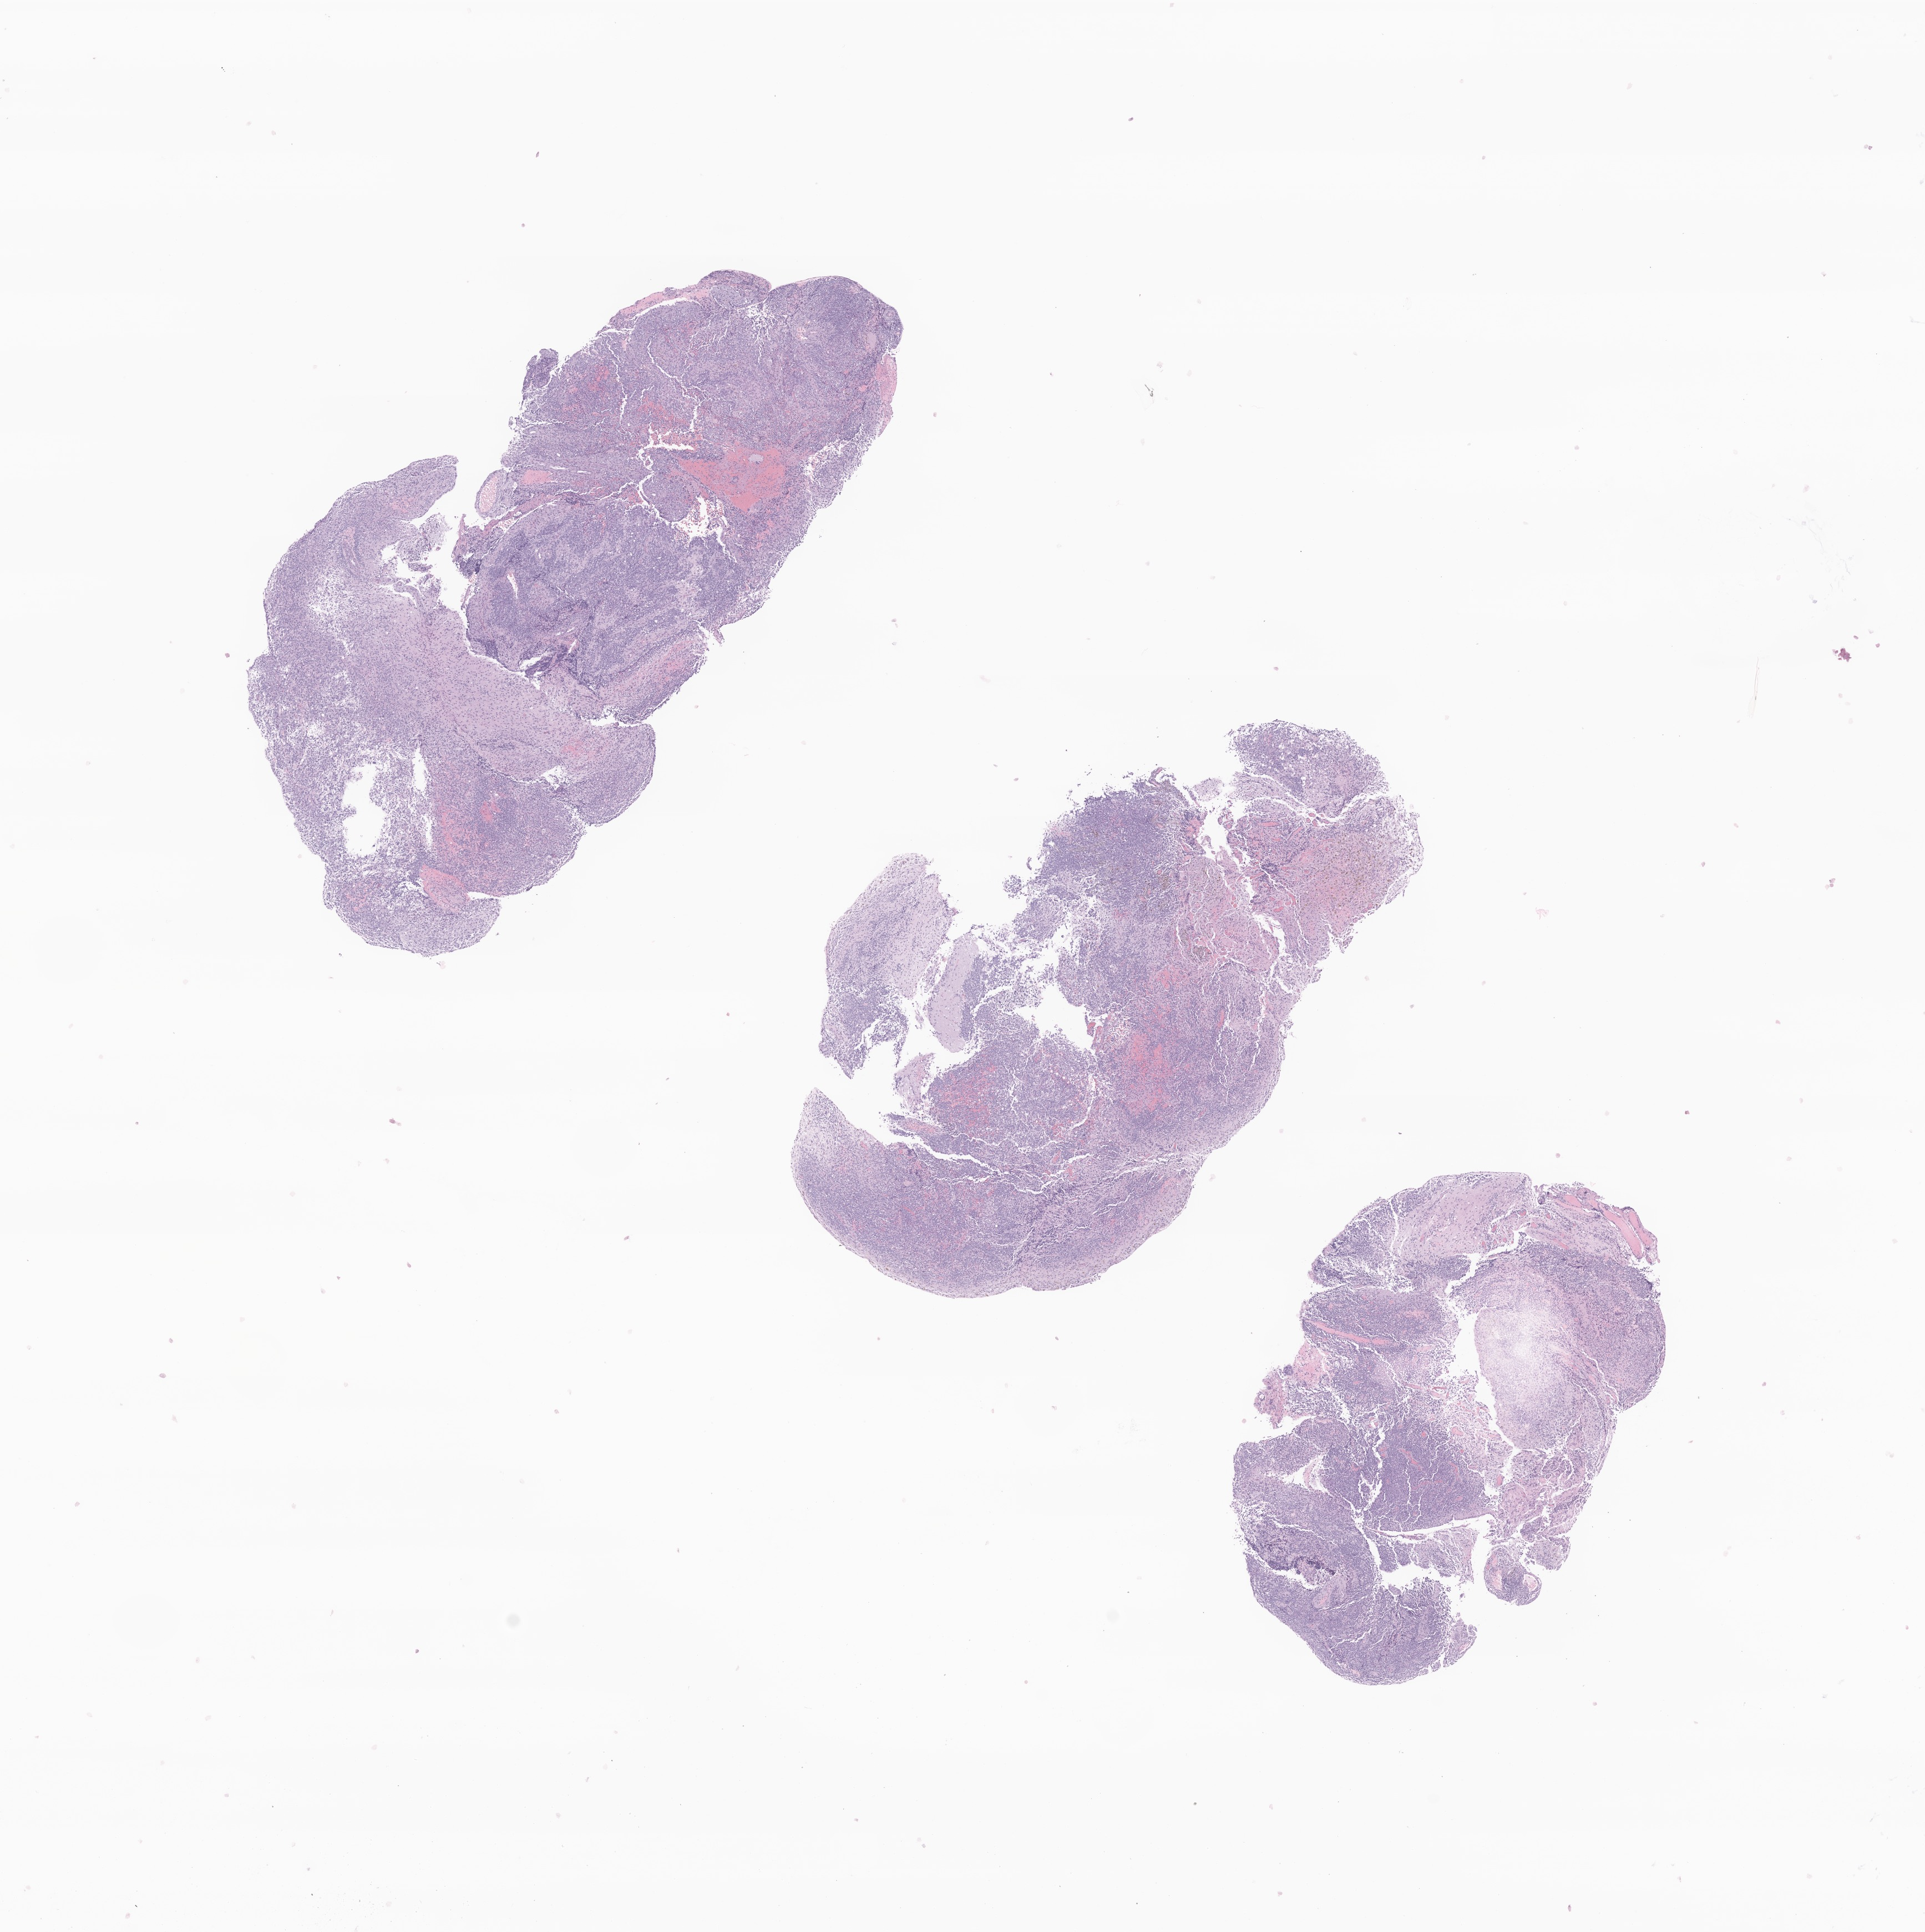
Haematoxylin and eosin whole-slide image of tumor tissue from the brain — a low-resolution overview of the entire scanned area, about 14.5 x 14.6 mm; formalin-fixed paraffin-embedded section. Patient female; age 82 months (6 years 10 months).
- recorded diagnosis: Neoplasm, uncertain whether benign or malignant